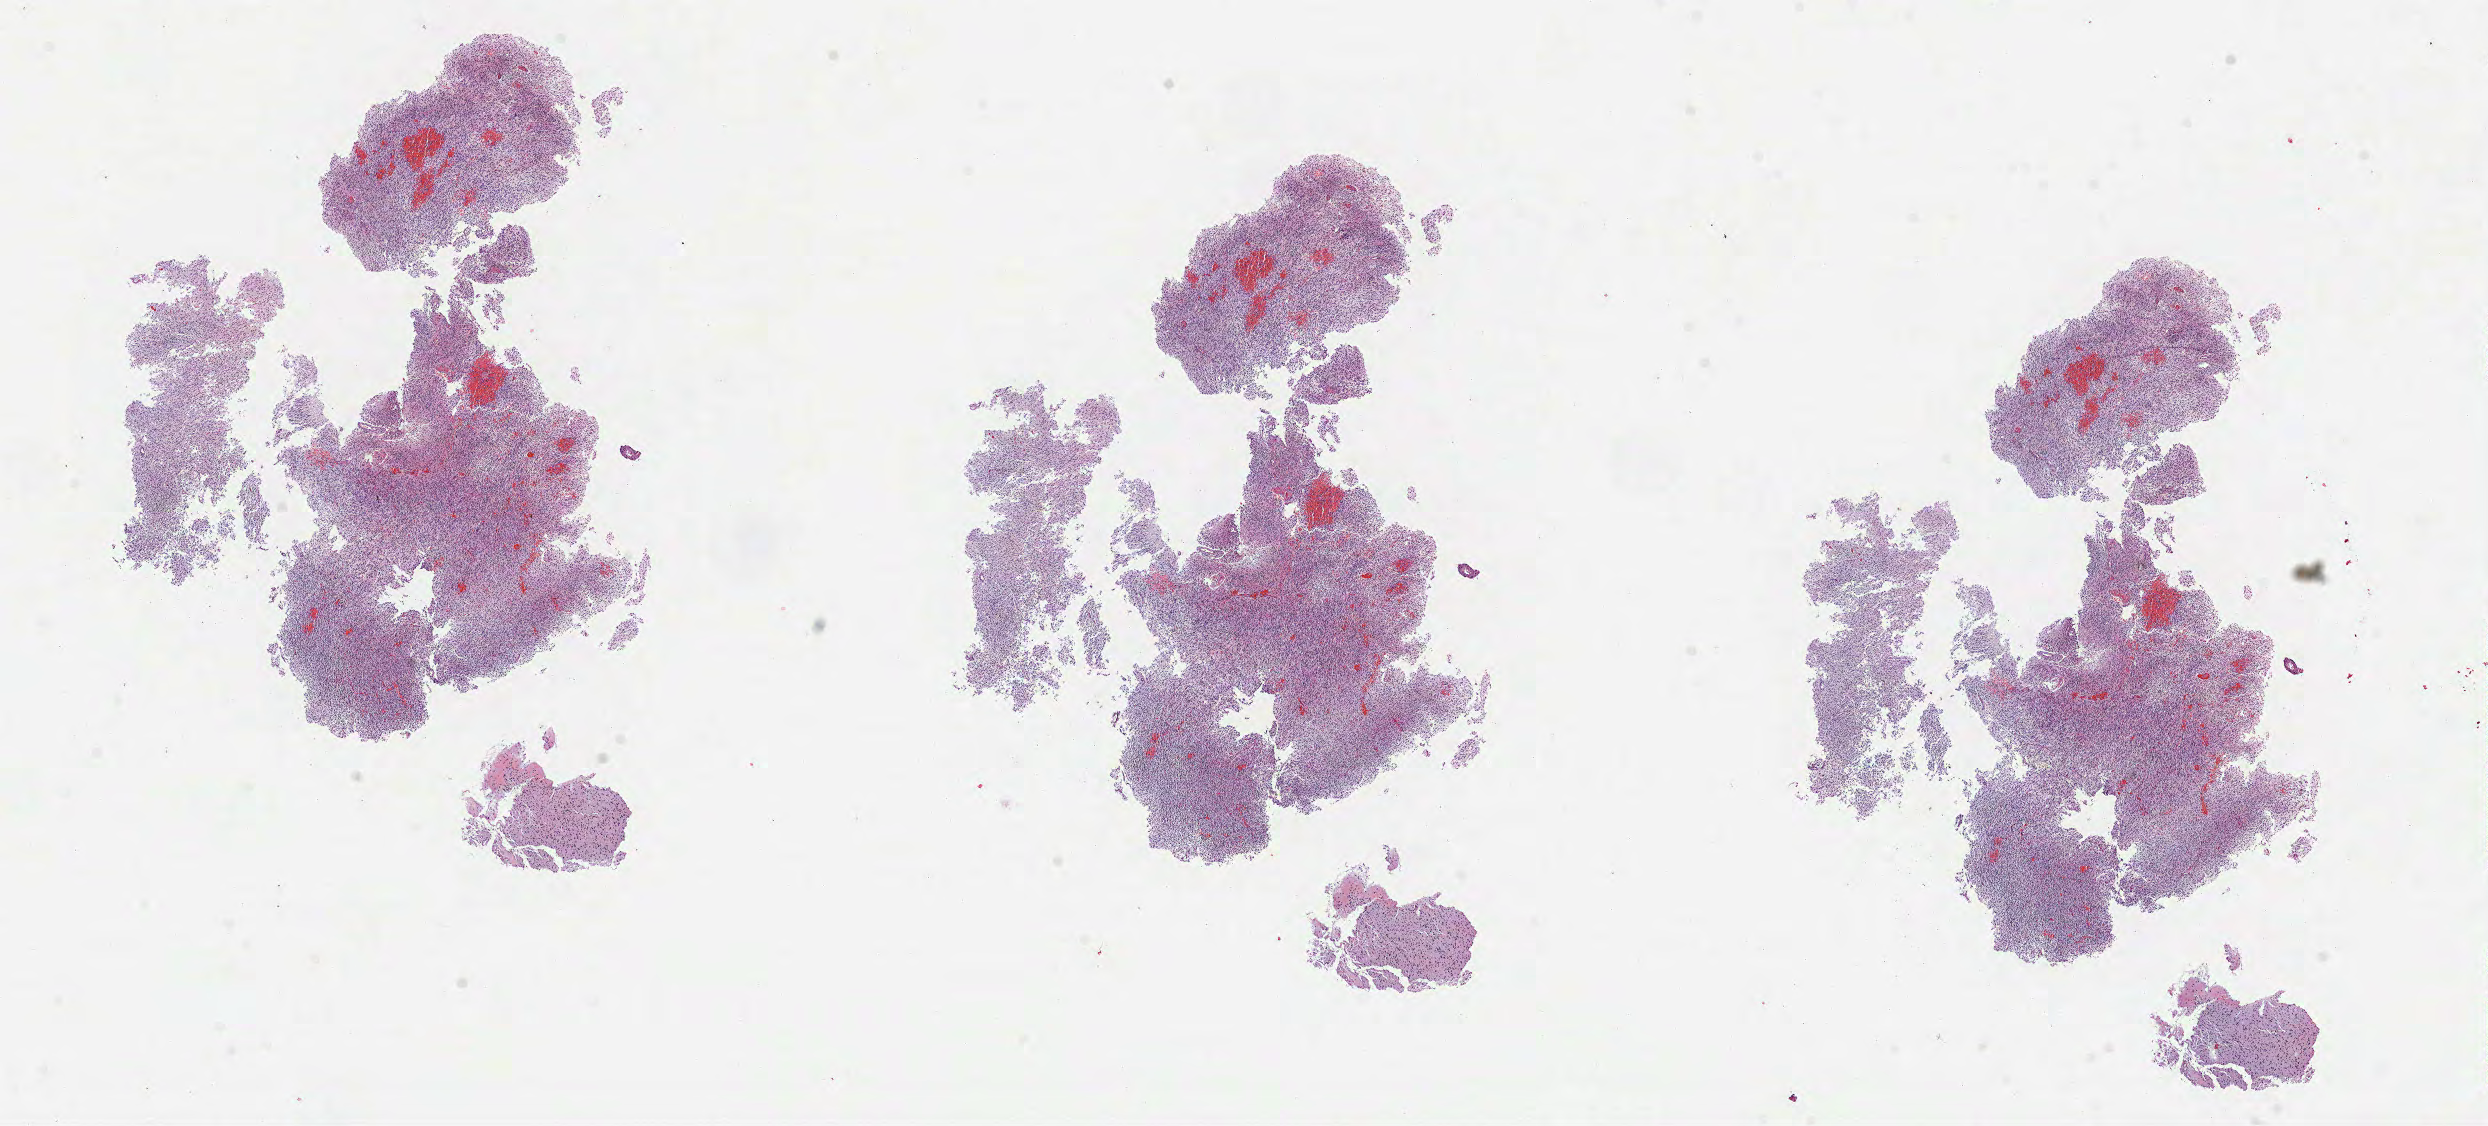
Hematoxylin and eosin (H&E) stained whole-slide image, low-resolution overview of the scanned area, about 20.1 x 9.1 mm. Formalin-fixed paraffin-embedded (FFPE) diagnostic section. Primary tumour sample from the brain. Patient: female, age at initial diagnosis 75 years.
Diagnosis: Glioblastoma.